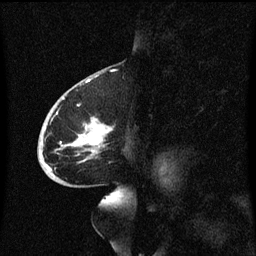
Breast MRI (dynamic contrast-enhanced), one sagittal slice. Slice 35 of 60 in the series (ordered by position). Dynamic contrast-enhanced series, image 2 of 3 at this slice position (ordered by acquisition). 1.5 T. TE 4.2 ms, TR 8.4 ms. 2 mm slice thickness. 256 × 256 image matrix, field of view 200 × 200 mm. Patient: female, 68 years. From the clinical record (not read from this slice): setting: breast cancer imaged before/during neoadjuvant chemotherapy; receptor status: triple-negative.
Structures marked on this image (semi-automatic segmentation, software-assisted and operator-edited):
- analysis volume of interest (the breast-tissue region the enhancement analysis was run in; not a lesion): bounding box <39,94,115,173> (left, top, right, bottom; pixels)
- tumour enhancement mask (voxels above the 70 % enhancement threshold inside the analysis volume of interest): <41,118,112,171>